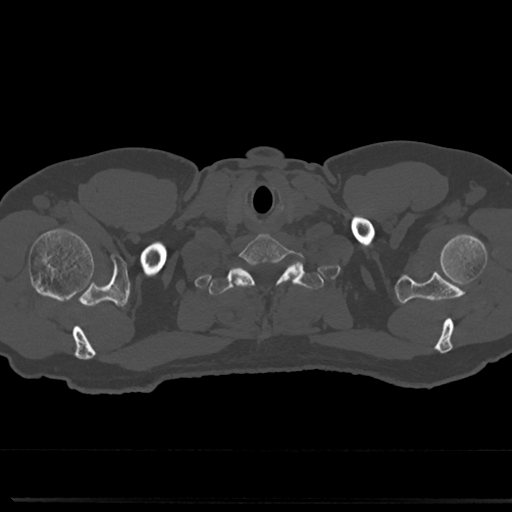
CT including the spine, one axial slice; position 690 of 817 along the scan axis; 120 kVp; bone window (W 1800 / L 400 HU); 512 × 512 image matrix. Patient: male, 61 years. Case-level facts recorded for this patient, not image findings: primary cancer: prostate.
Annotated regions visible in this slice (semi-automatic segmentation, software-assisted and operator-edited):
- T1 vertebra: box from (x=211, y=262) to (x=318, y=344) px